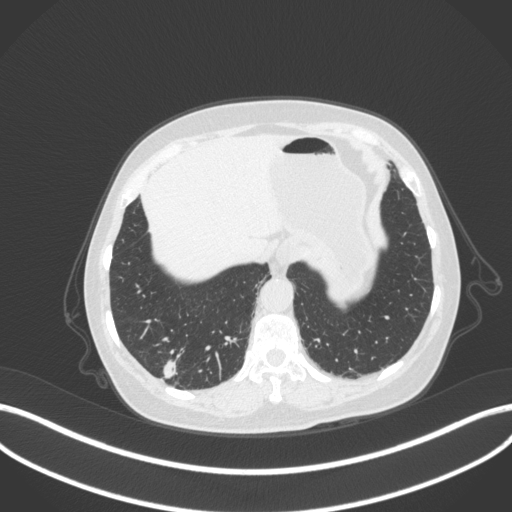
Chest CT, one axial slice. Position 50 of 340 along the scan axis. 120 kVp. Lung window (W 1500 / L -600 HU). 512 × 512 image matrix, field of view 400 × 400 mm. Patient: female, 69 years. From the clinical record (not read from this slice): clinical TNM (as recorded): T1b N0 M0.
Structures marked on this image (bounding box drawn by a radiologist):
- lung tumour (recorded histology: adenocarcinoma): box from (x=160, y=357) to (x=178, y=381) px